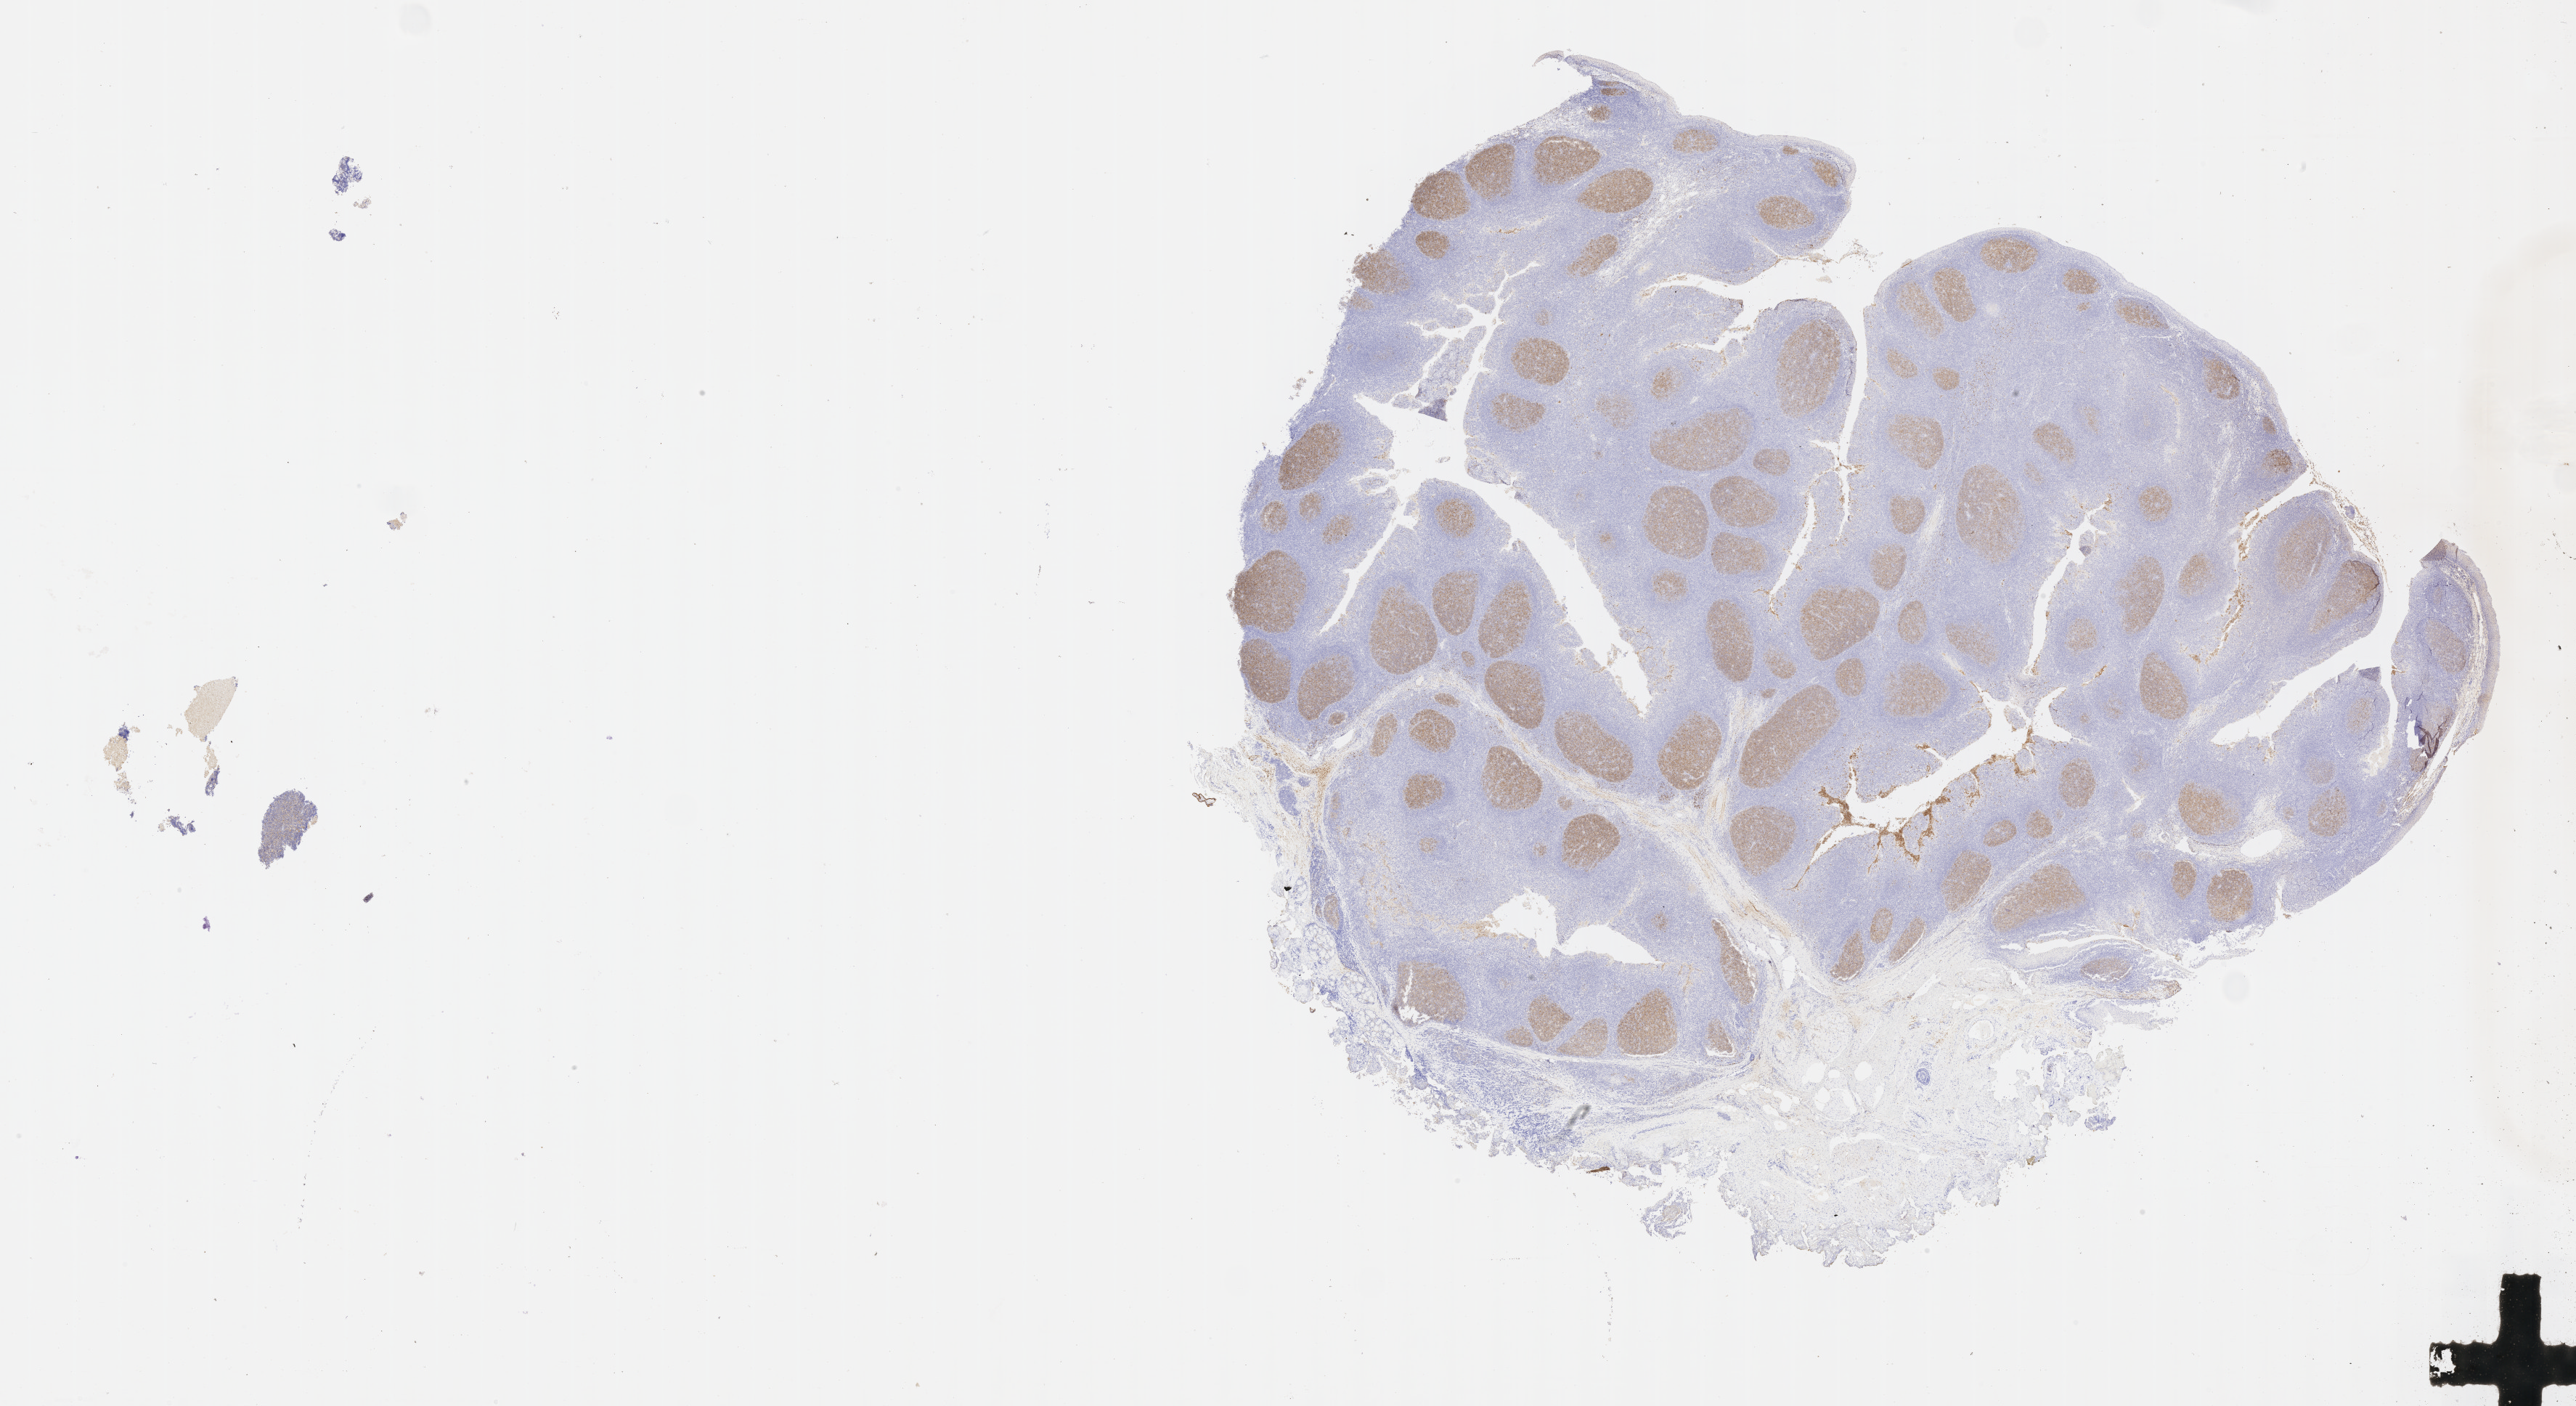
Immunohistochemistry (IHC) whole-slide image stained for CD10 — a low-resolution overview of the entire scanned area, about 28.7 x 15.7 mm, tumor tissue, anatomic site: abdominal lymph node. Male, age 5 years at initial diagnosis.
Diagnosis: Diffuse large B-cell lymphoma, NOS.